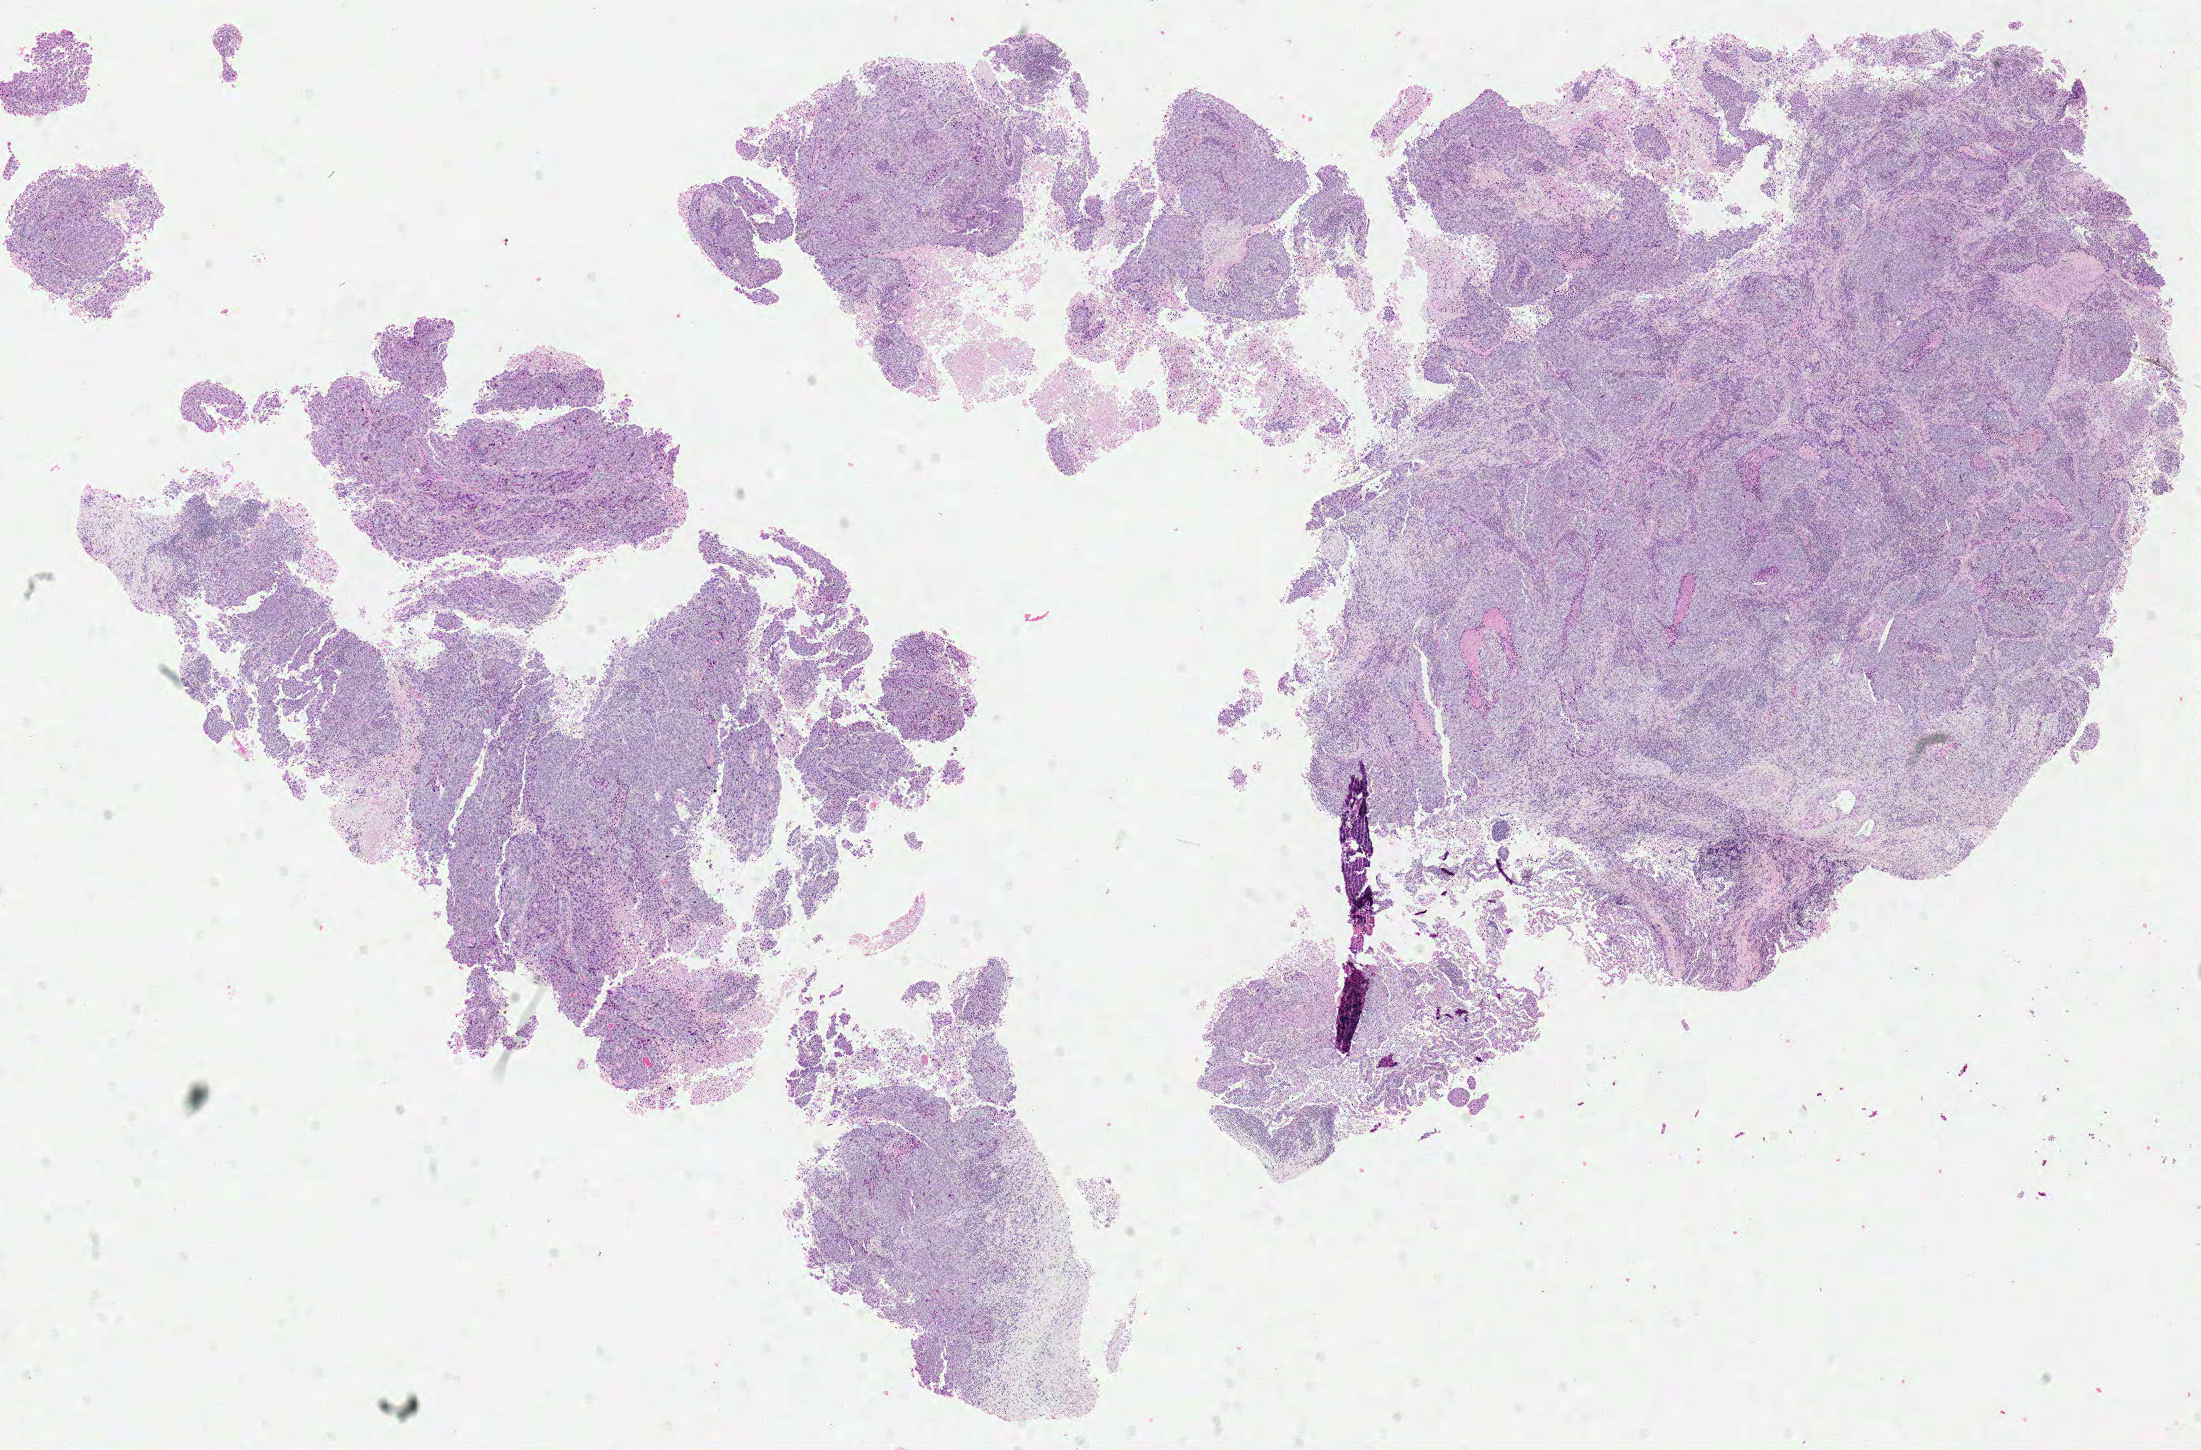
Whole-slide histology image, H&E — low-resolution overview of the scanned area, about 17.3 x 11.4 mm (slide scanned at 40x). Formalin-fixed paraffin-embedded (FFPE) diagnostic section. Primary tumour sample from the lung. Male patient; age at initial diagnosis 71 years.
- diagnosis: Squamous cell carcinoma, NOS (upper lobe, lung)
- laterality: left
- AJCC pathologic stage: IB